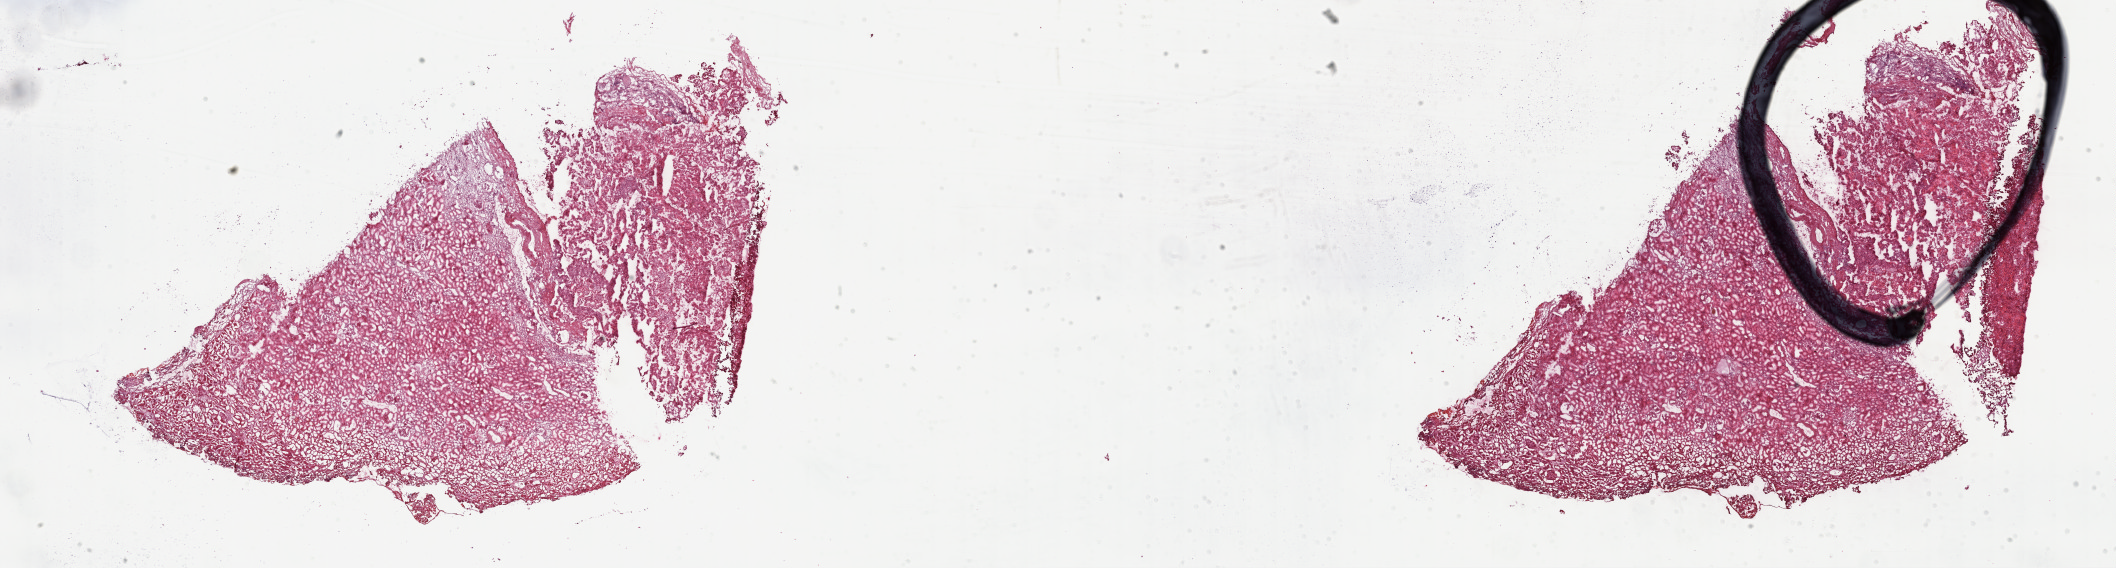
H&E-stained whole-slide image — low-resolution overview of the scanned area, about 34.2 x 9.2 mm. Frozen section from the top of the tissue portion. Kidney, primary tumour sample. Male patient; age at initial diagnosis 64 years. Slide review estimates, as recorded: tumour cells 100%, tumour nuclei 75%, normal cells 0%, stromal cells 0%, necrosis 0%. Inflammatory infiltration, as recorded: lymphocyte infiltration 1%, monocyte infiltration 5%, neutrophil infiltration 0%.
Diagnosis: Papillary adenocarcinoma, NOS.